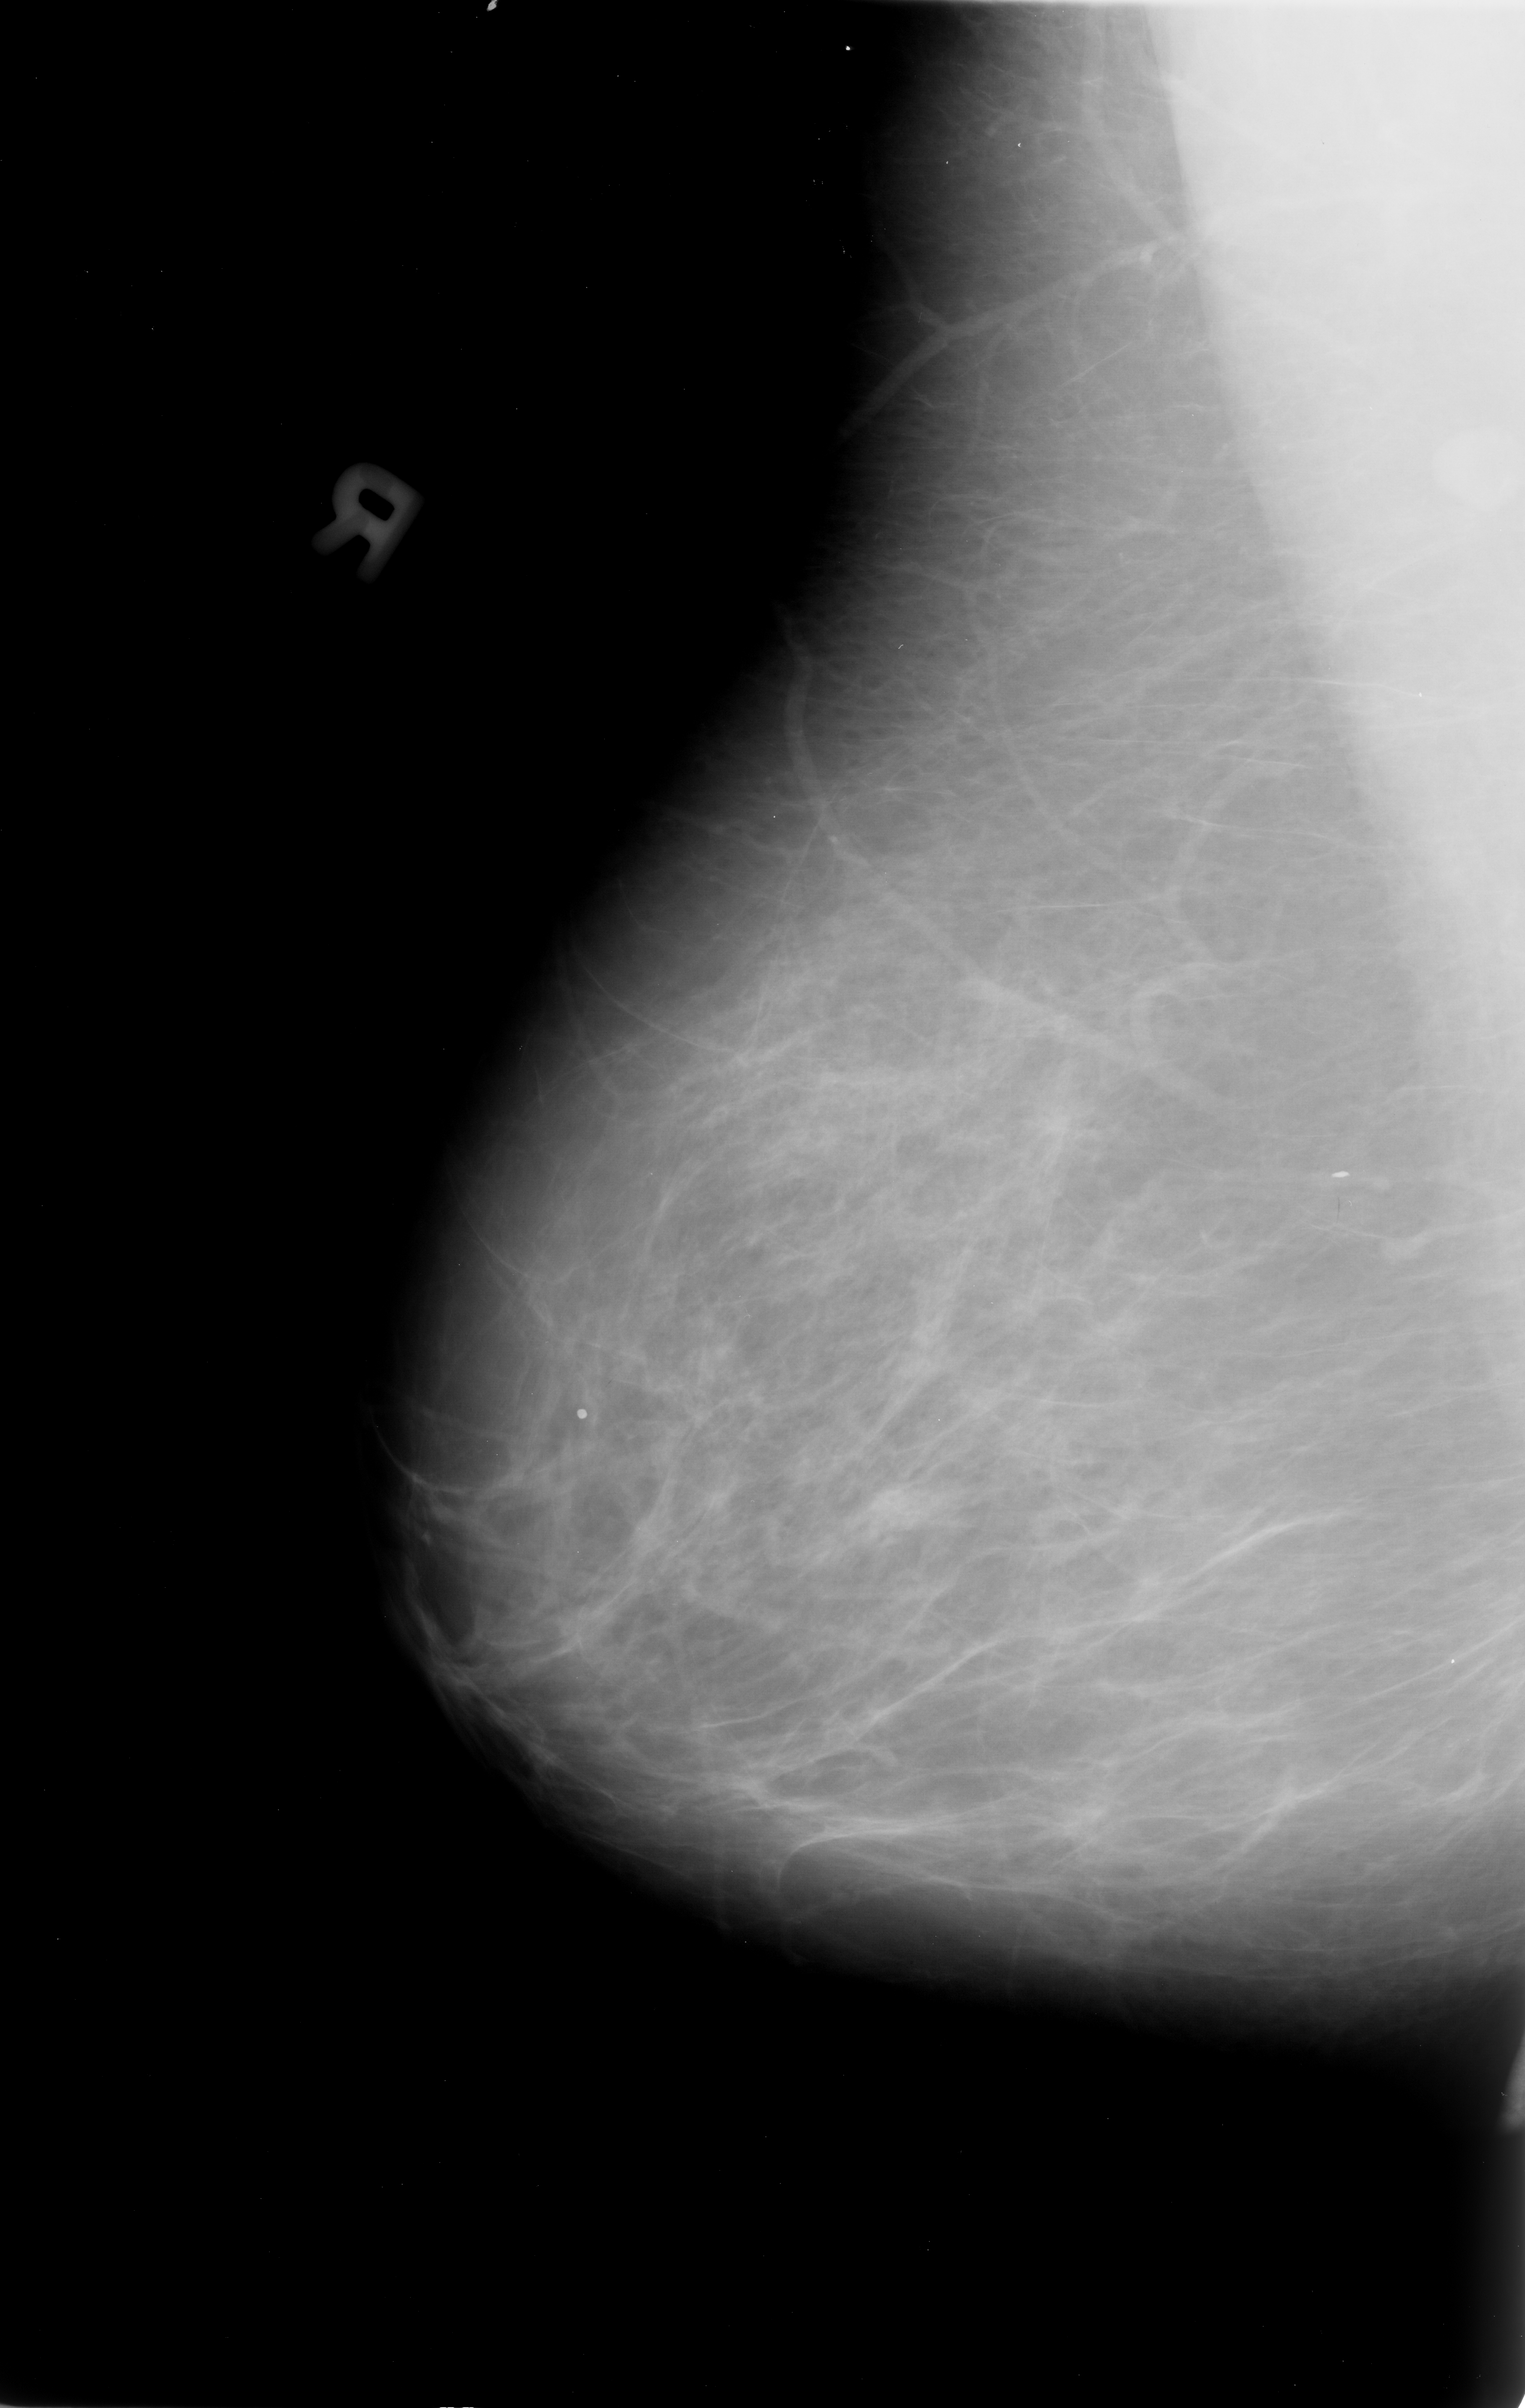
Scanned film-screen mammogram; right breast; mediolateral oblique (MLO) view; BI-RADS breast density category 1 (scale 1–4).
Marked findings (only marked abnormalities are described; nothing is implied about the rest of the image): Finding 1 of 2: calcifications, morphology coarse; BI-RADS assessment category 2; benign without callback (not worked up further). Finding 2 of 2: calcifications, morphology vascular; BI-RADS assessment category 2; benign; no additional work-up was recommended (benign without callback).